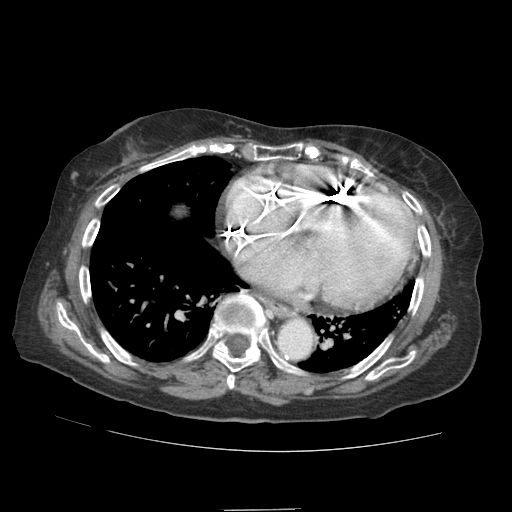
Contrast-enhanced abdominal CT (liver protocol), one axial slice; slice 85 of 89 in the series (ordered by position); 140 kVp; soft-tissue window (W 400 / L 40 HU); 2.5 mm slice thickness; 512 × 512 image matrix, field of view 360 × 360 mm. From the clinical record (not read from this slice): diagnosis: hepatocellular carcinoma (patient treated with transarterial chemoembolisation; whether this scan precedes or follows treatment is not stated here); TNM stage (as recorded): Stage-II.
Outlined on this slice (semi-automatically segmented with operator editing):
- liver parenchyma outside the tumour (the mass and vessels are separate outlines, so this box may not span the whole liver): bounding box <175,206,186,215> (left, top, right, bottom; pixels)